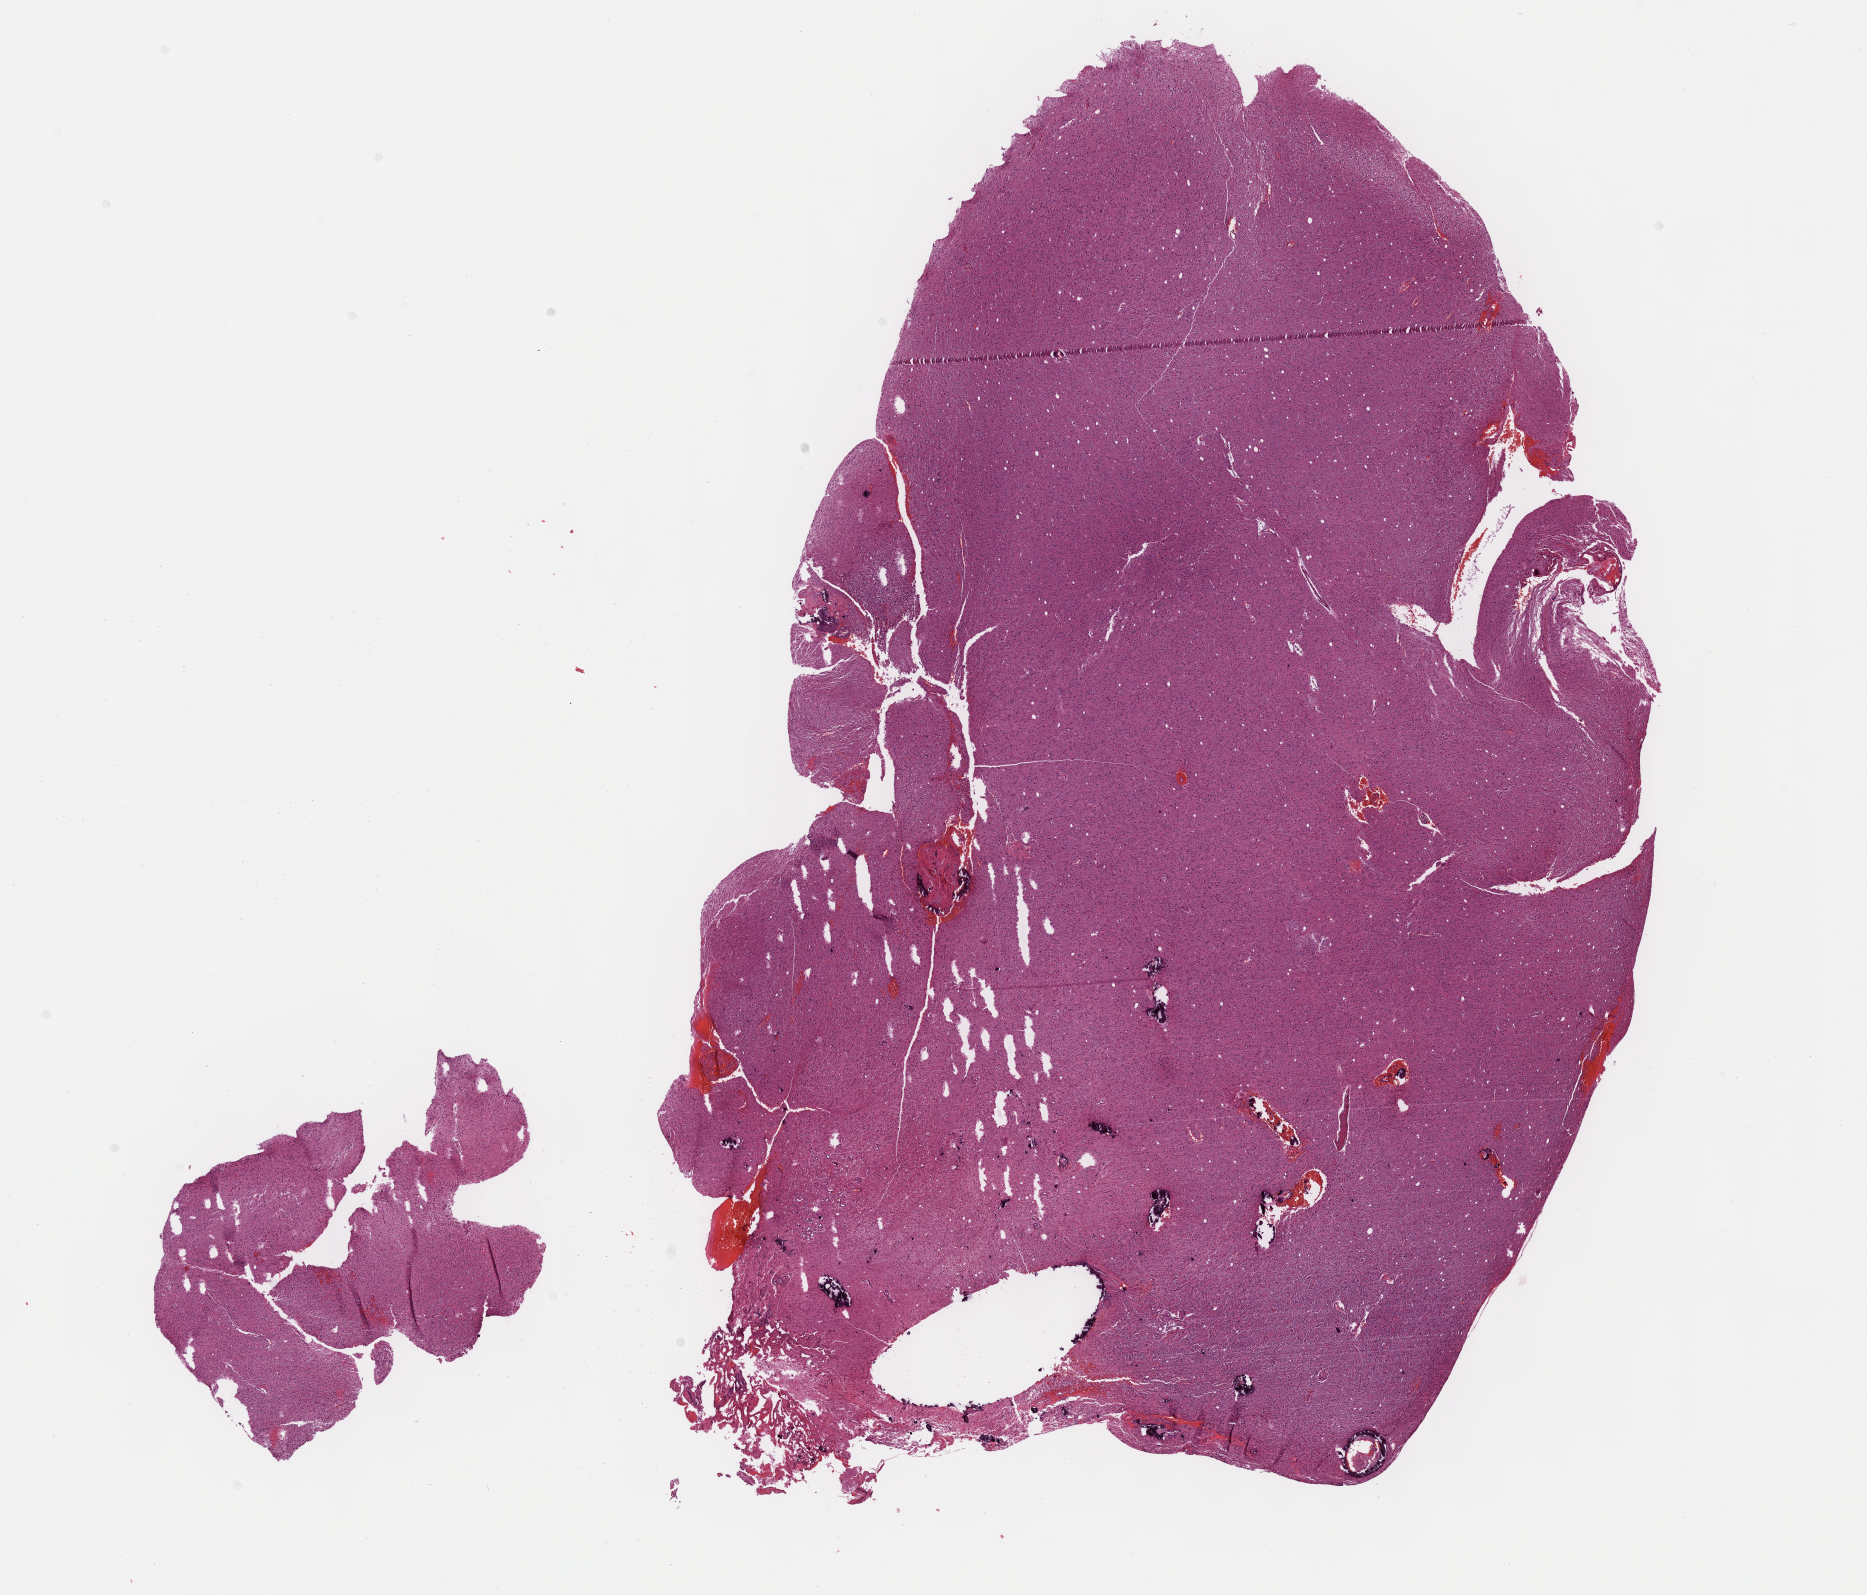
Digitized H&E tissue section (whole slide), a low-resolution overview of the entire scanned area, about 15.1 x 12.9 mm; formalin-fixed paraffin-embedded (FFPE) diagnostic section; brain, primary tumour sample. Male patient; age at initial diagnosis 40 years. Histologic grade: G3 (poorly differentiated).
- diagnosis: Oligodendroglioma, anaplastic
- laterality: left